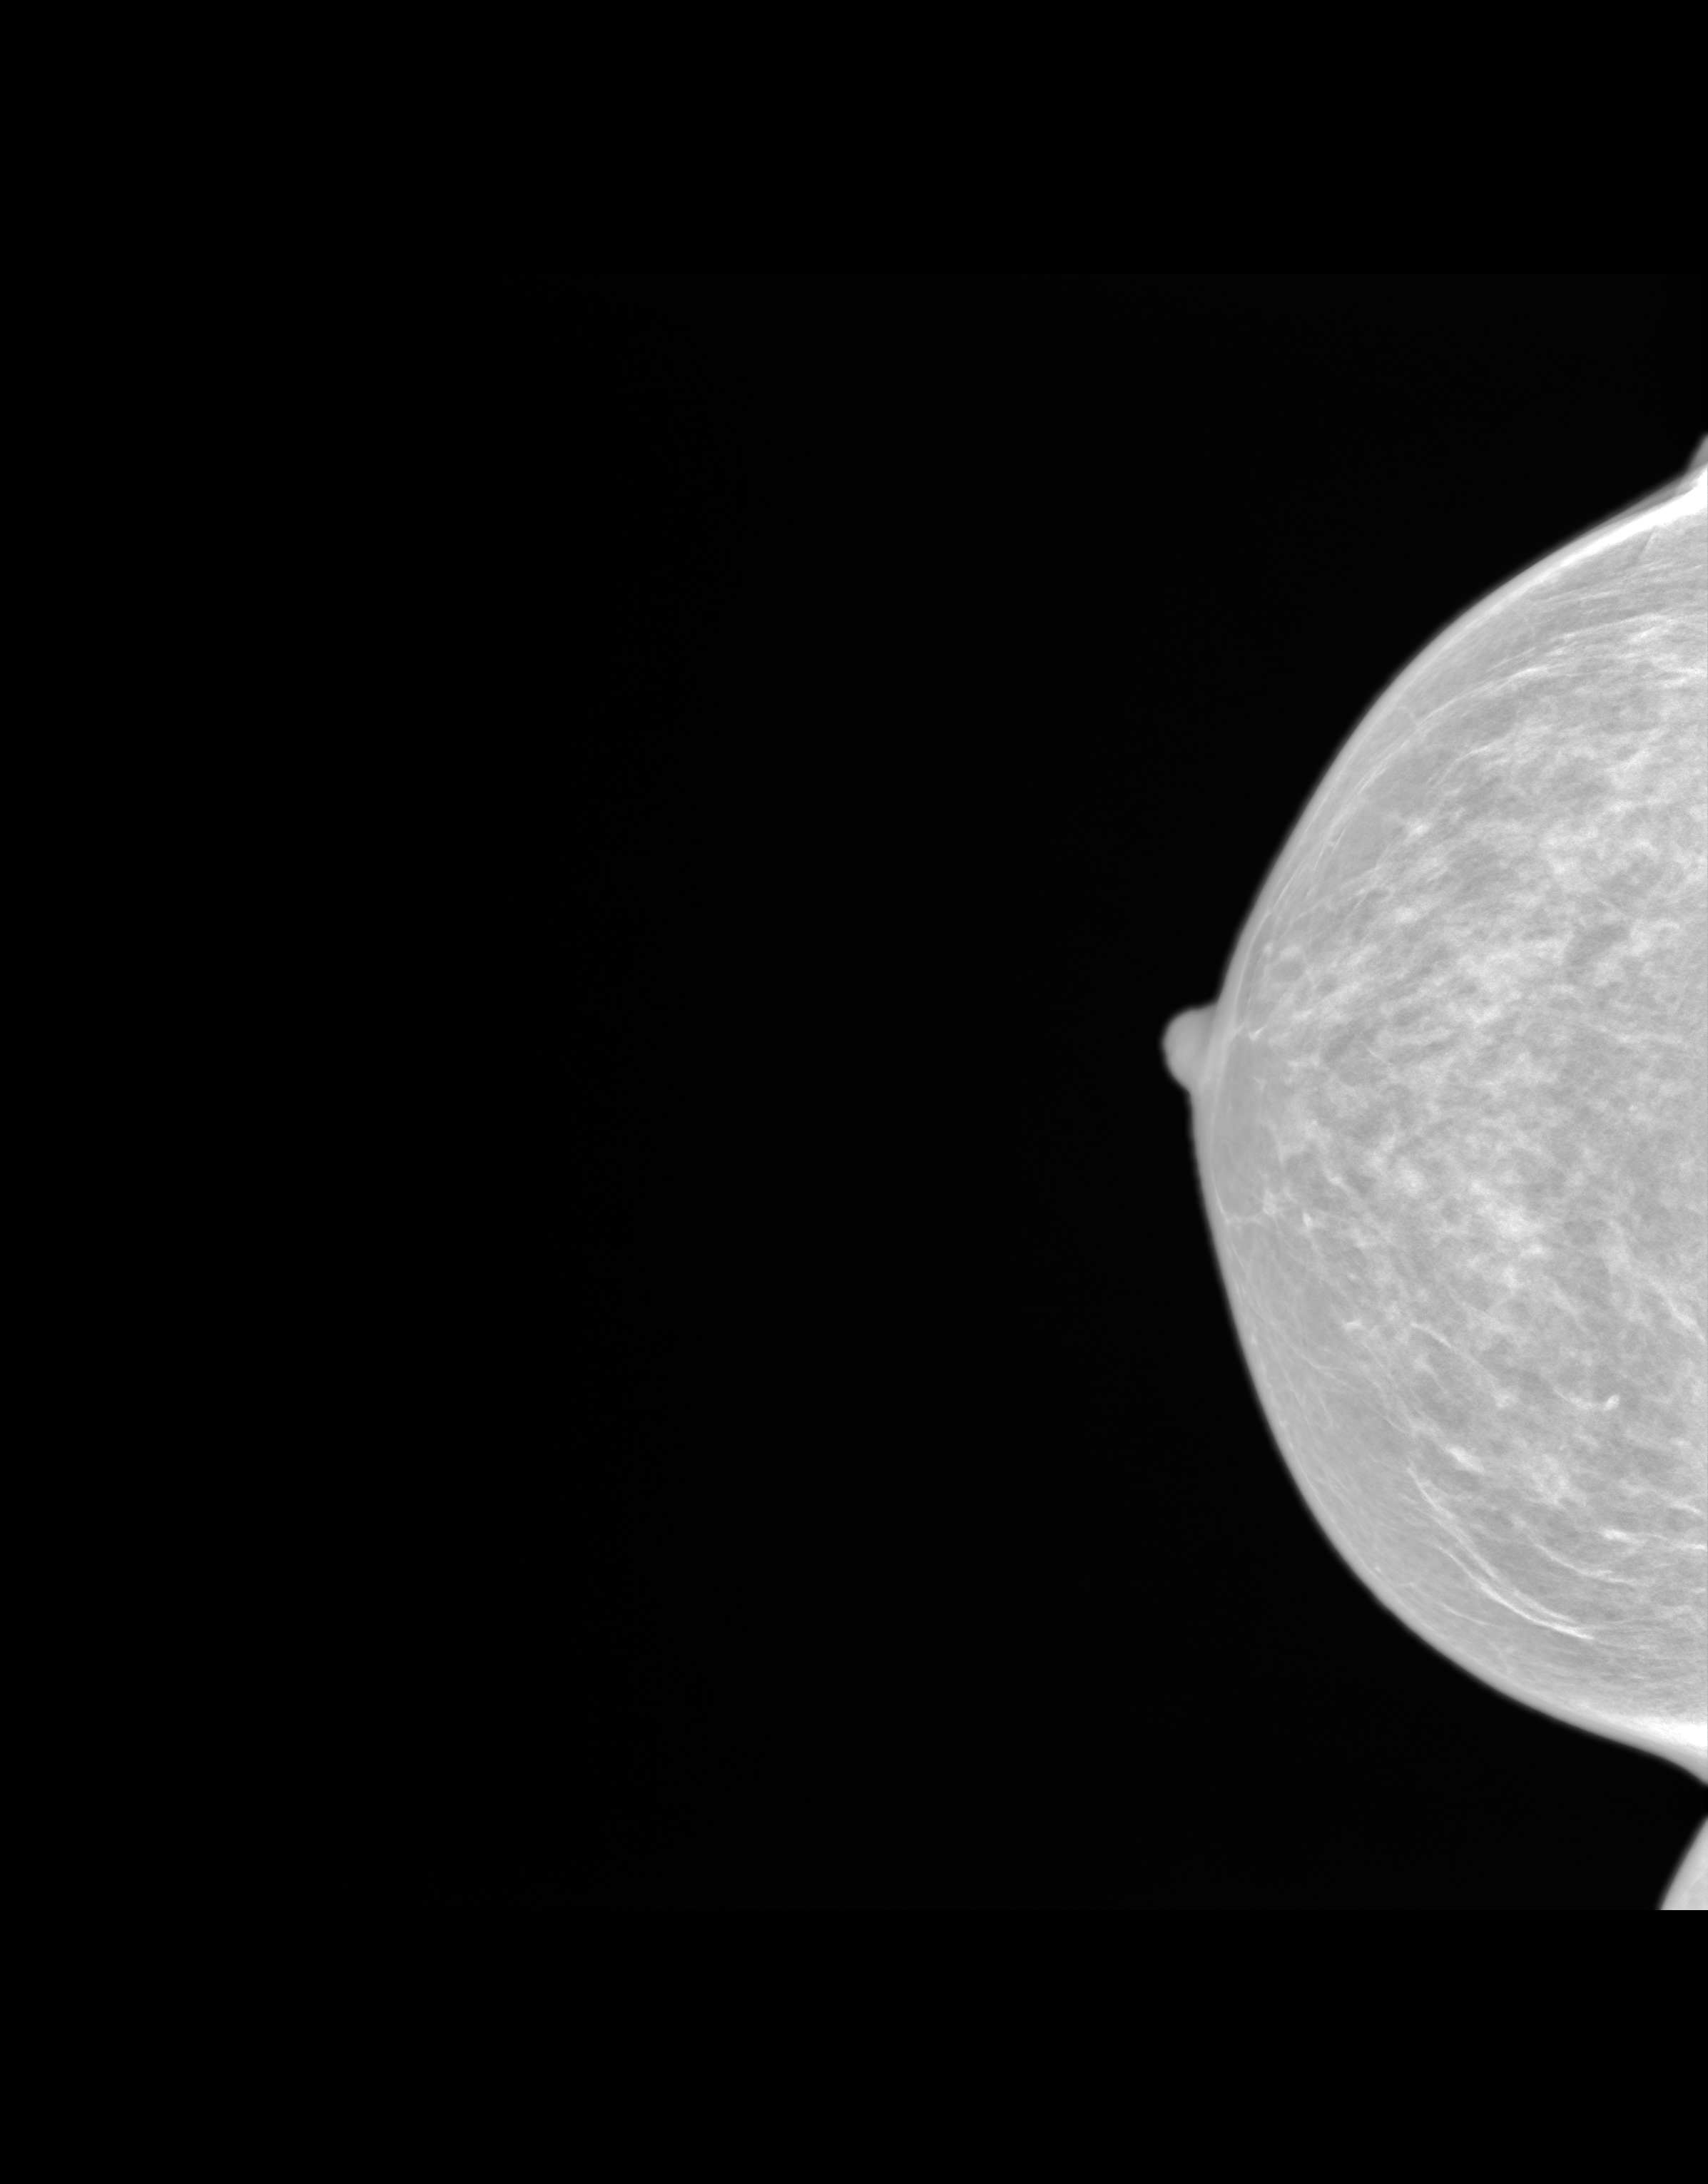
Annual screening mammography examination, system: SenoIris_1SP2(440). Female patient, age 70 years.
Image type: synthesized 2-D view from tomosynthesis. Breast: right. Projection: cranio-caudal projection.